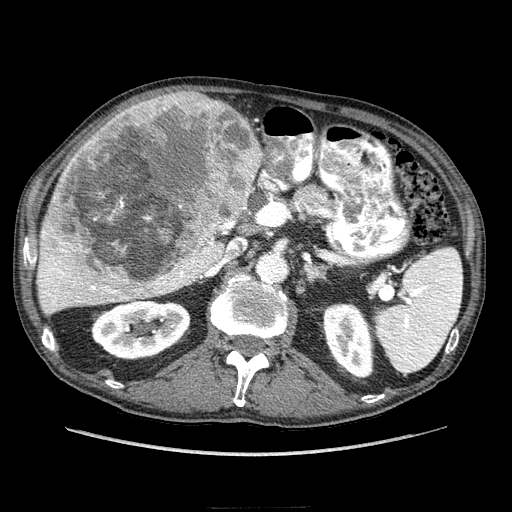
Contrast-enhanced abdominal CT (liver protocol), one axial slice. Position 133 of 218 along the scan axis. Soft-tissue window (W 400 / L 40 HU). 2.5 mm slice thickness. 512 × 512 image matrix, field of view 380 × 380 mm. From the clinical record (not read from this slice): diagnosis: hepatocellular carcinoma (patient treated with transarterial chemoembolisation; whether this scan precedes or follows treatment is not stated here); TNM stage (as recorded): Stage-IIIA; Child-Pugh class: A; tumour differentiation: well differentiated; tumour nodularity: multinodular.
Annotated regions visible in this slice (semi-automatic segmentation, software-assisted and operator-edited):
- liver parenchyma outside the tumour (the mass and vessels are separate outlines, so this box may not span the whole liver): bounding box [x1, y1, x2, y2] px = [36, 98, 262, 314]
- mass: [40, 91, 261, 297]
- liver vessels: [40, 222, 234, 306]